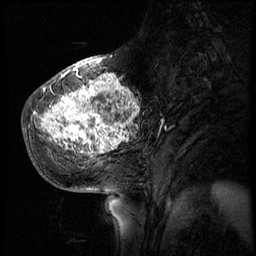
Breast MRI (dynamic contrast-enhanced), one sagittal slice. Slice 22 of 56 in the series (ordered by position). 4 images stored at this slice position (order not interpretable as contrast timing). 1.5 T. TE 4.2 ms, TR 8.9 ms. 2.5 mm slice thickness. 256 × 256 image matrix. Female patient, age 51 years. Case-level facts recorded for this patient, not image findings: setting: breast cancer imaged before/during neoadjuvant chemotherapy; receptor status: triple-negative.
Outlined on this slice (semi-automatic segmentation, software-assisted and operator-edited):
- analysis volume of interest (the breast-tissue region the enhancement analysis was run in; not a lesion): box from (x=30, y=70) to (x=150, y=173) px
- tumour enhancement mask (voxels above the 140 % enhancement threshold inside the analysis volume of interest): (x=34, y=74)–(x=141, y=155)